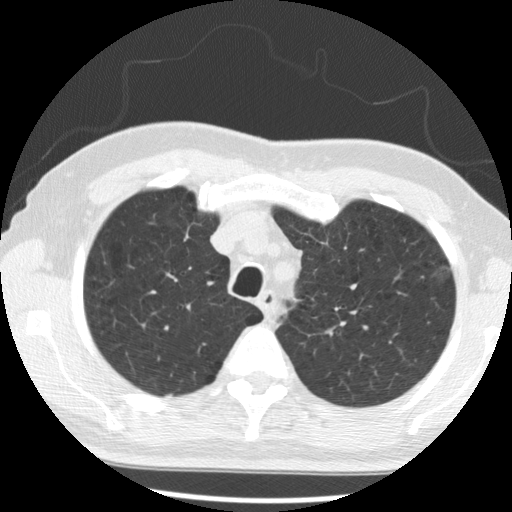
Low-dose screening chest CT, axial slice; second annual screen; lung window (W 1500 / L -600 HU); 2.5 mm slice thickness; standard (soft-tissue) reconstruction kernel (STANDARD); slice 62 of 285 in the series; 512 × 512 image matrix, field of view 340 × 340 mm. Male, age 68 years at enrolment. Current smoker at enrolment.
Expert-annotated lung lesion, bounding box (x1, y1, x2, y2) in pixels: (418, 261, 460, 294). Reader record for this screening exam (exam-level; its link to the box is not recorded): non-calcified nodule or mass ≥4 mm, left upper lobe, 15 × 11 mm, poorly defined margins, ground glass attenuation, pre-existing on the prior screen: yes; interval growth: yes. Participant outcome: lung cancer diagnosed 278 days after this screen — bronchiolo-alveolar adenocarcinoma, NOS, left upper lobe, moderately differentiated (G2), stage IA (AJCC 6th edition), 17 mm at pathology.